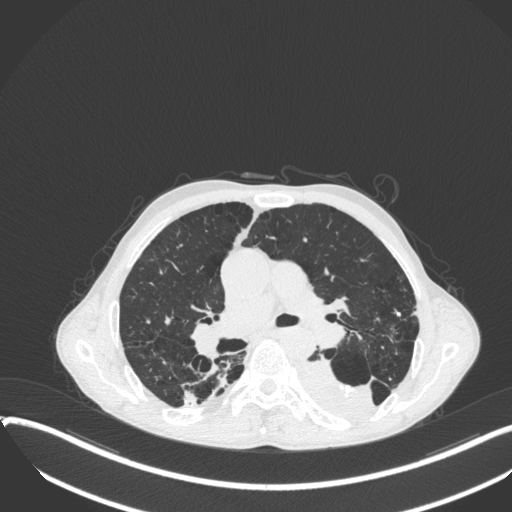
Chest CT, one axial slice; slice 229 of 400 in the series (ordered by position); reconstruction kernel B31f; 120 kVp; lung window (W 1500 / L -600 HU); 1 mm slice thickness; 512 × 512 image matrix, field of view 400 × 400 mm. Patient: male, 57 years. Case-level facts recorded for this patient, not image findings: clinical TNM (as recorded): T4 N0 M0.
Annotated regions visible in this slice (rectangle marked by the reading radiologist):
- lung tumour (recorded histology: squamous cell carcinoma): bounding box [x1, y1, x2, y2] px = [295, 348, 379, 420]